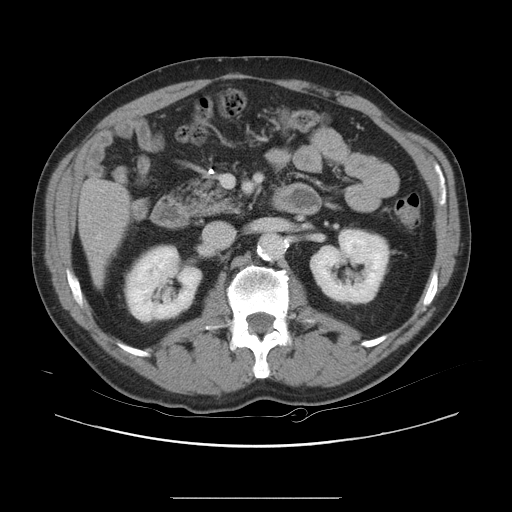
Contrast-enhanced abdominal CT, one axial slice. Position 7 of 40 along the scan axis. 120 kVp. Soft-tissue window (W 400 / L 40 HU). 5 mm slice thickness. 512 × 512 image matrix, field of view 408 × 408 mm. Male patient, age 64 years. From the clinical record (not read from this slice): diagnosis: colorectal cancer liver metastases, imaged before liver resection.
Structures marked on this image (expert manual segmentation):
- hepatic veins: box from (x=97, y=235) to (x=101, y=239) px
- liver: (x=80, y=183)–(x=129, y=280)